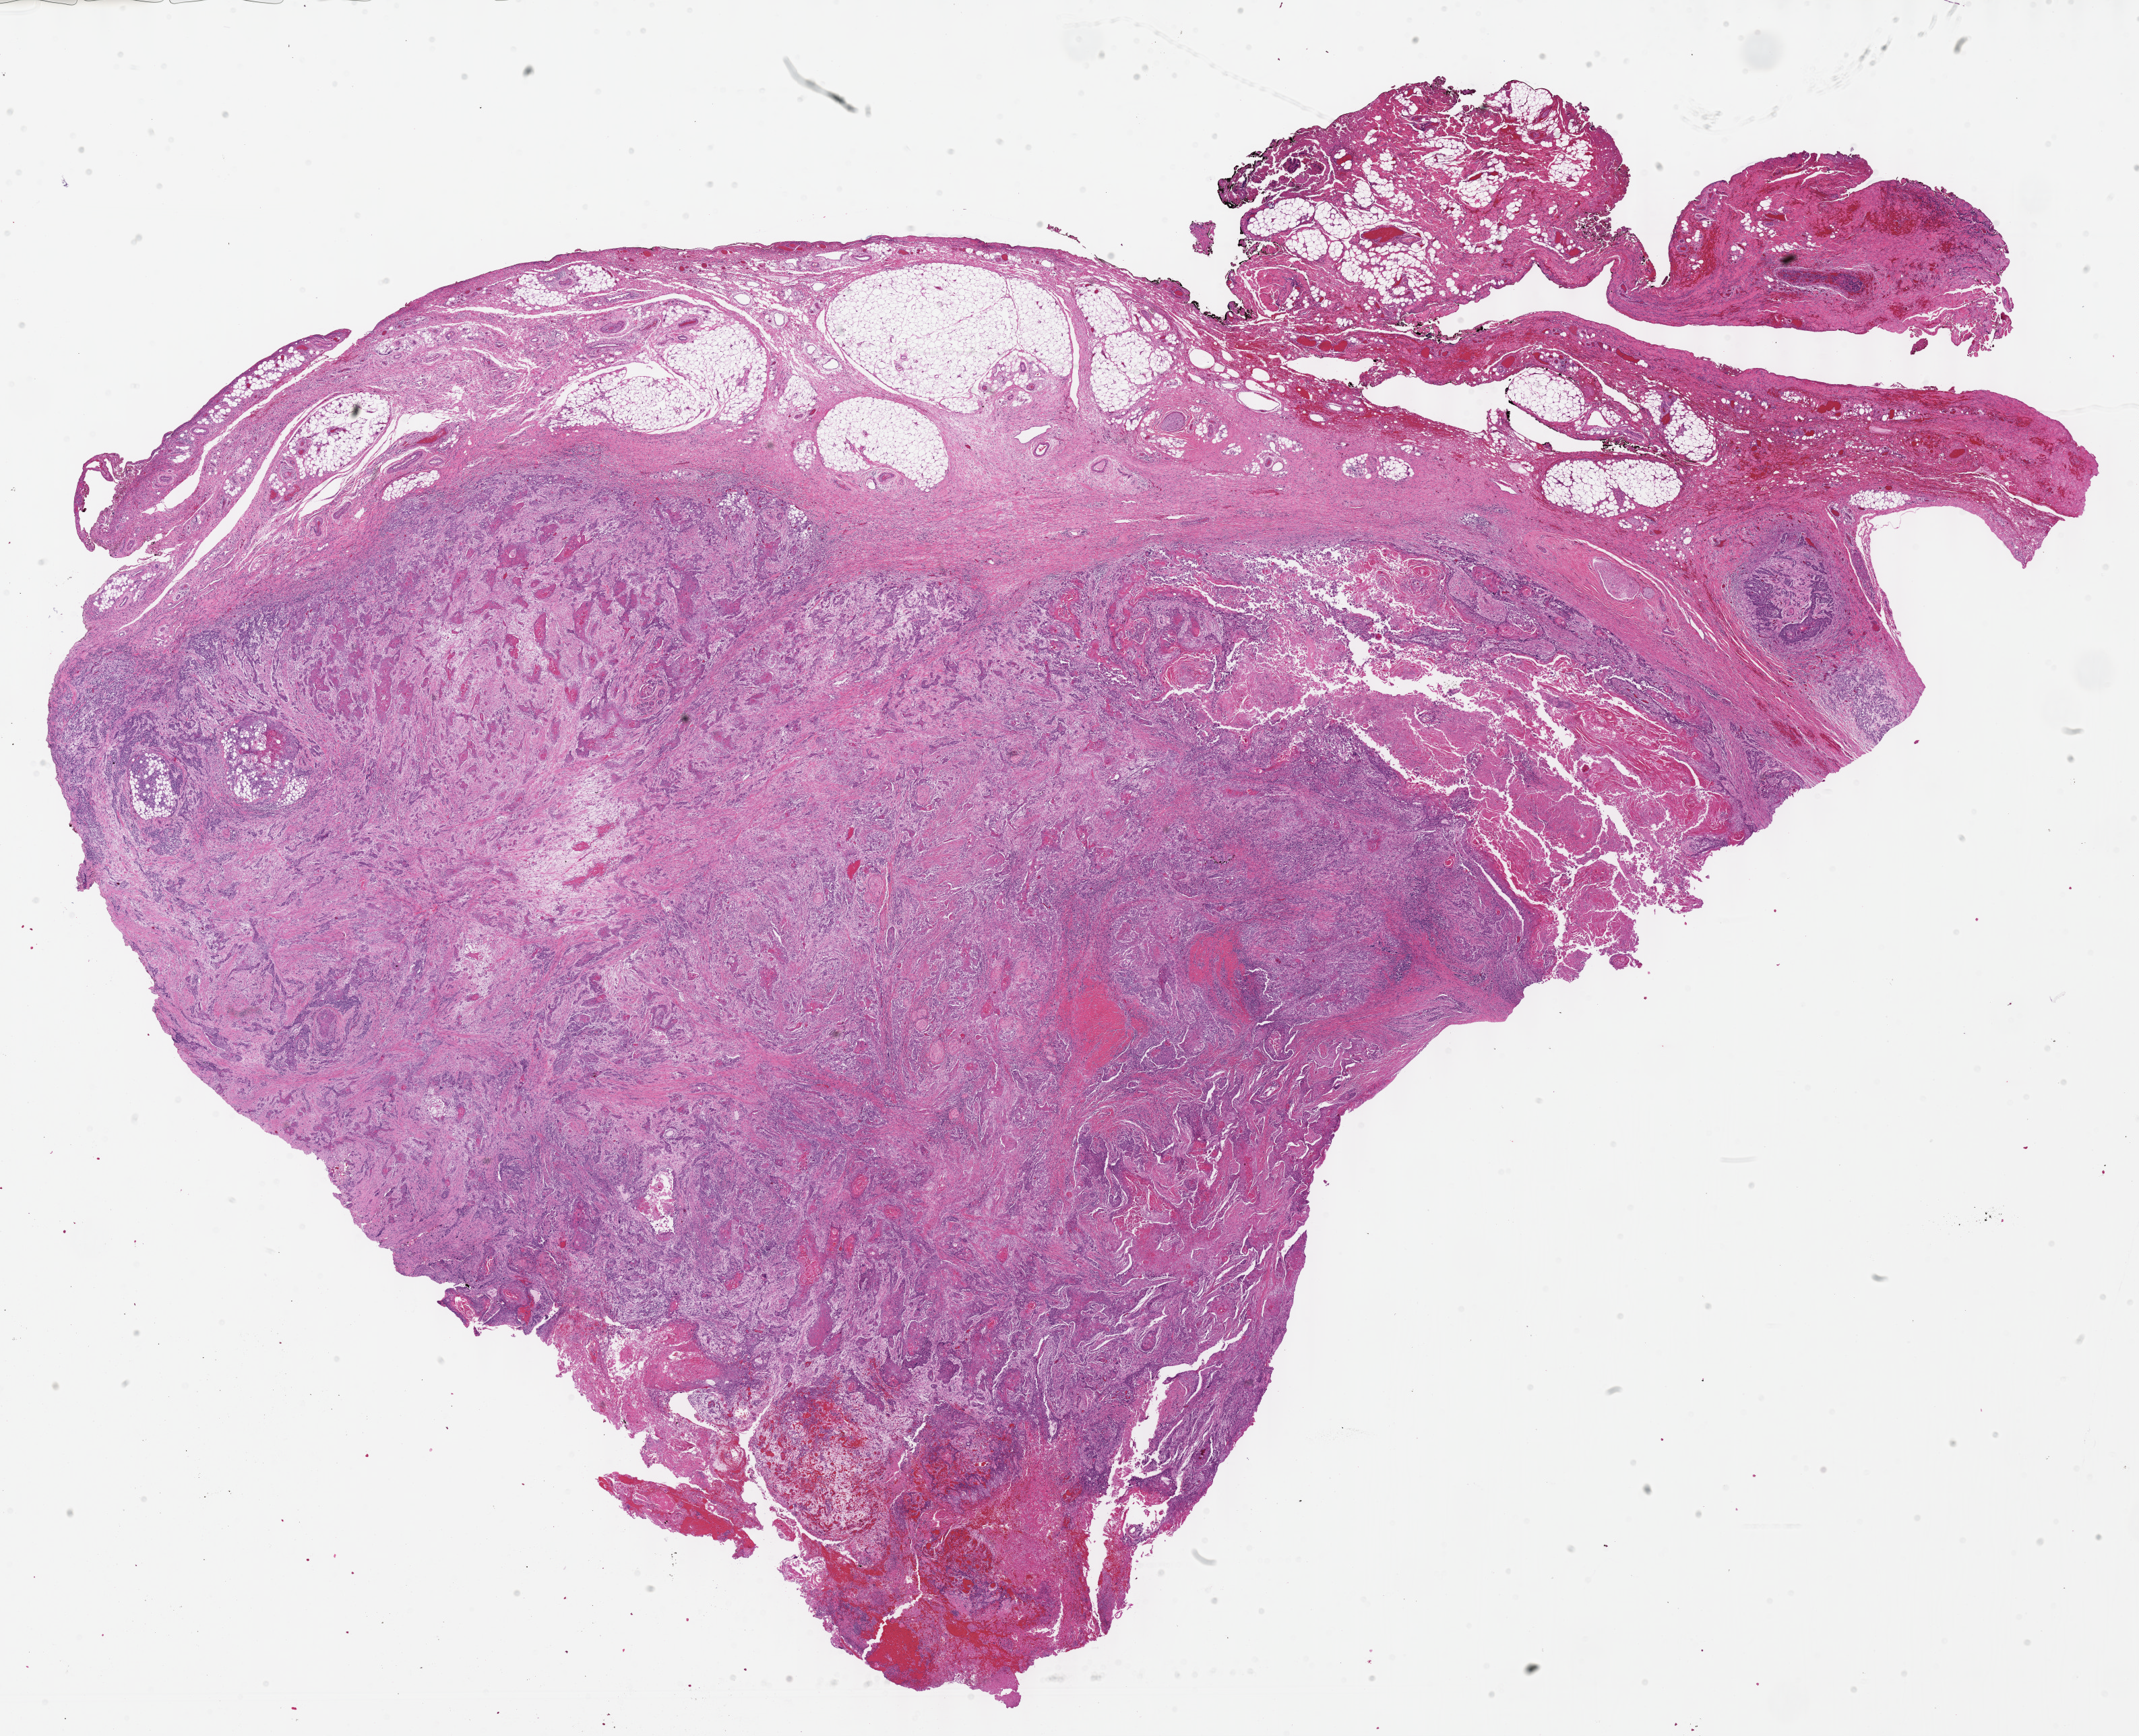
Digitized H&E tissue section (whole slide), low-resolution overview of the scanned area, about 25.7 x 20.8 mm. Formalin-fixed paraffin-embedded (FFPE) diagnostic section. Head and neck, primary tumour sample. Male patient; age at initial diagnosis 68 years. Histologic grade: G3 (poorly differentiated).
Diagnosis: Squamous cell carcinoma, NOS (larynx, NOS). TNM: T4a N2c M0. AJCC pathologic stage: IVA.